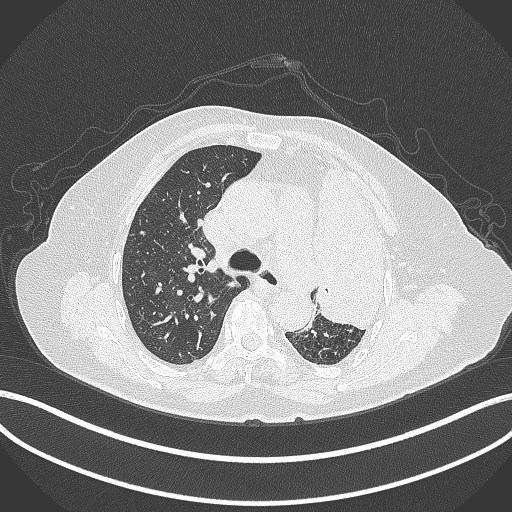
Chest CT, one axial slice. Position 262 of 399 along the scan axis. Reconstruction kernel B70f. 120 kVp. Lung window (W 1500 / L -600 HU). 1 mm slice thickness. 512 × 512 image matrix, field of view 400 × 400 mm. Patient: female, 75 years. From the clinical record (not read from this slice): clinical TNM (as recorded): T3 N3 M1.
Annotated regions visible in this slice (rectangle marked by the reading radiologist):
- lung tumour (recorded histology: adenocarcinoma): bounding box (x1, y1, x2, y2) in pixels: (311, 161, 393, 334)